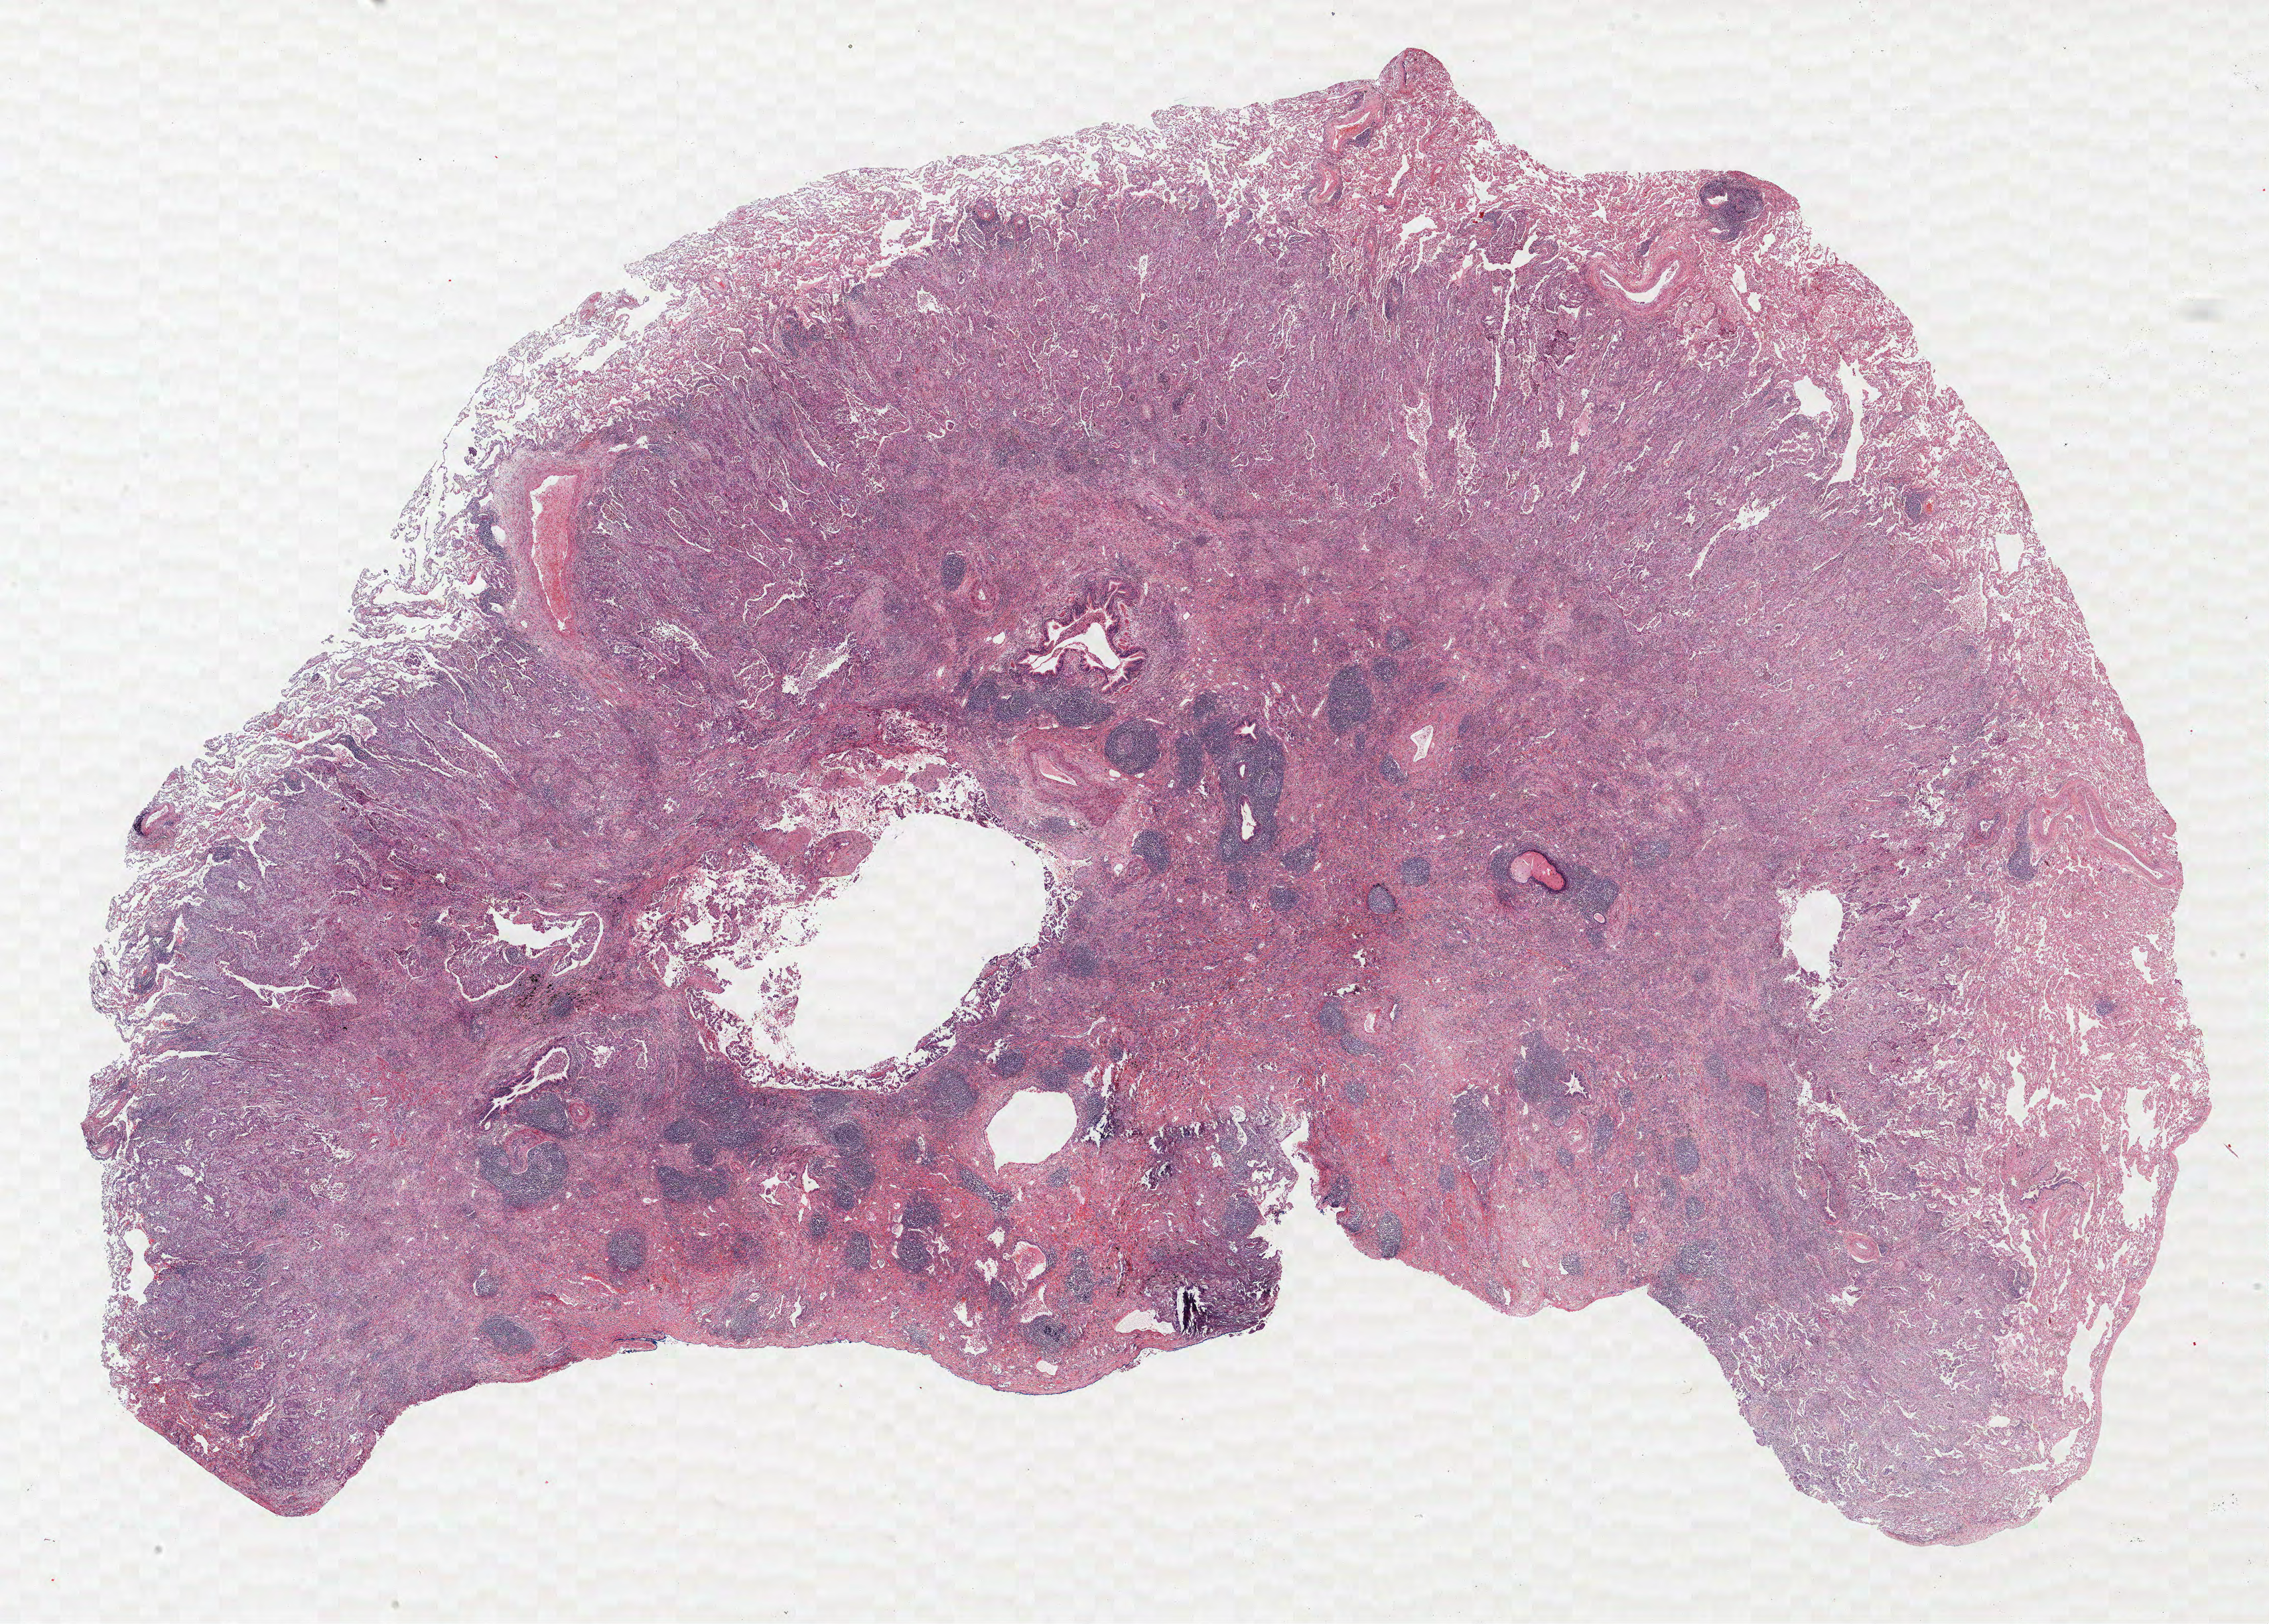
Hematoxylin and eosin (H&E) stained whole-slide image — a low-resolution overview of the entire scanned area, about 27.4 x 19.6 mm, formalin-fixed paraffin-embedded (FFPE) section, lung. Female patient, aged 68 at enrolment. Current smoker at enrolment. Grade: moderately differentiated (G2).
Primary tumour location (clinical record): left lower lobe. Participant's lung-cancer diagnosis: Adenocarcinoma, NOS (ICD-O-3 8140/3). Stage (AJCC 6th edition): IB. Tumour size (pathology): 40 mm.